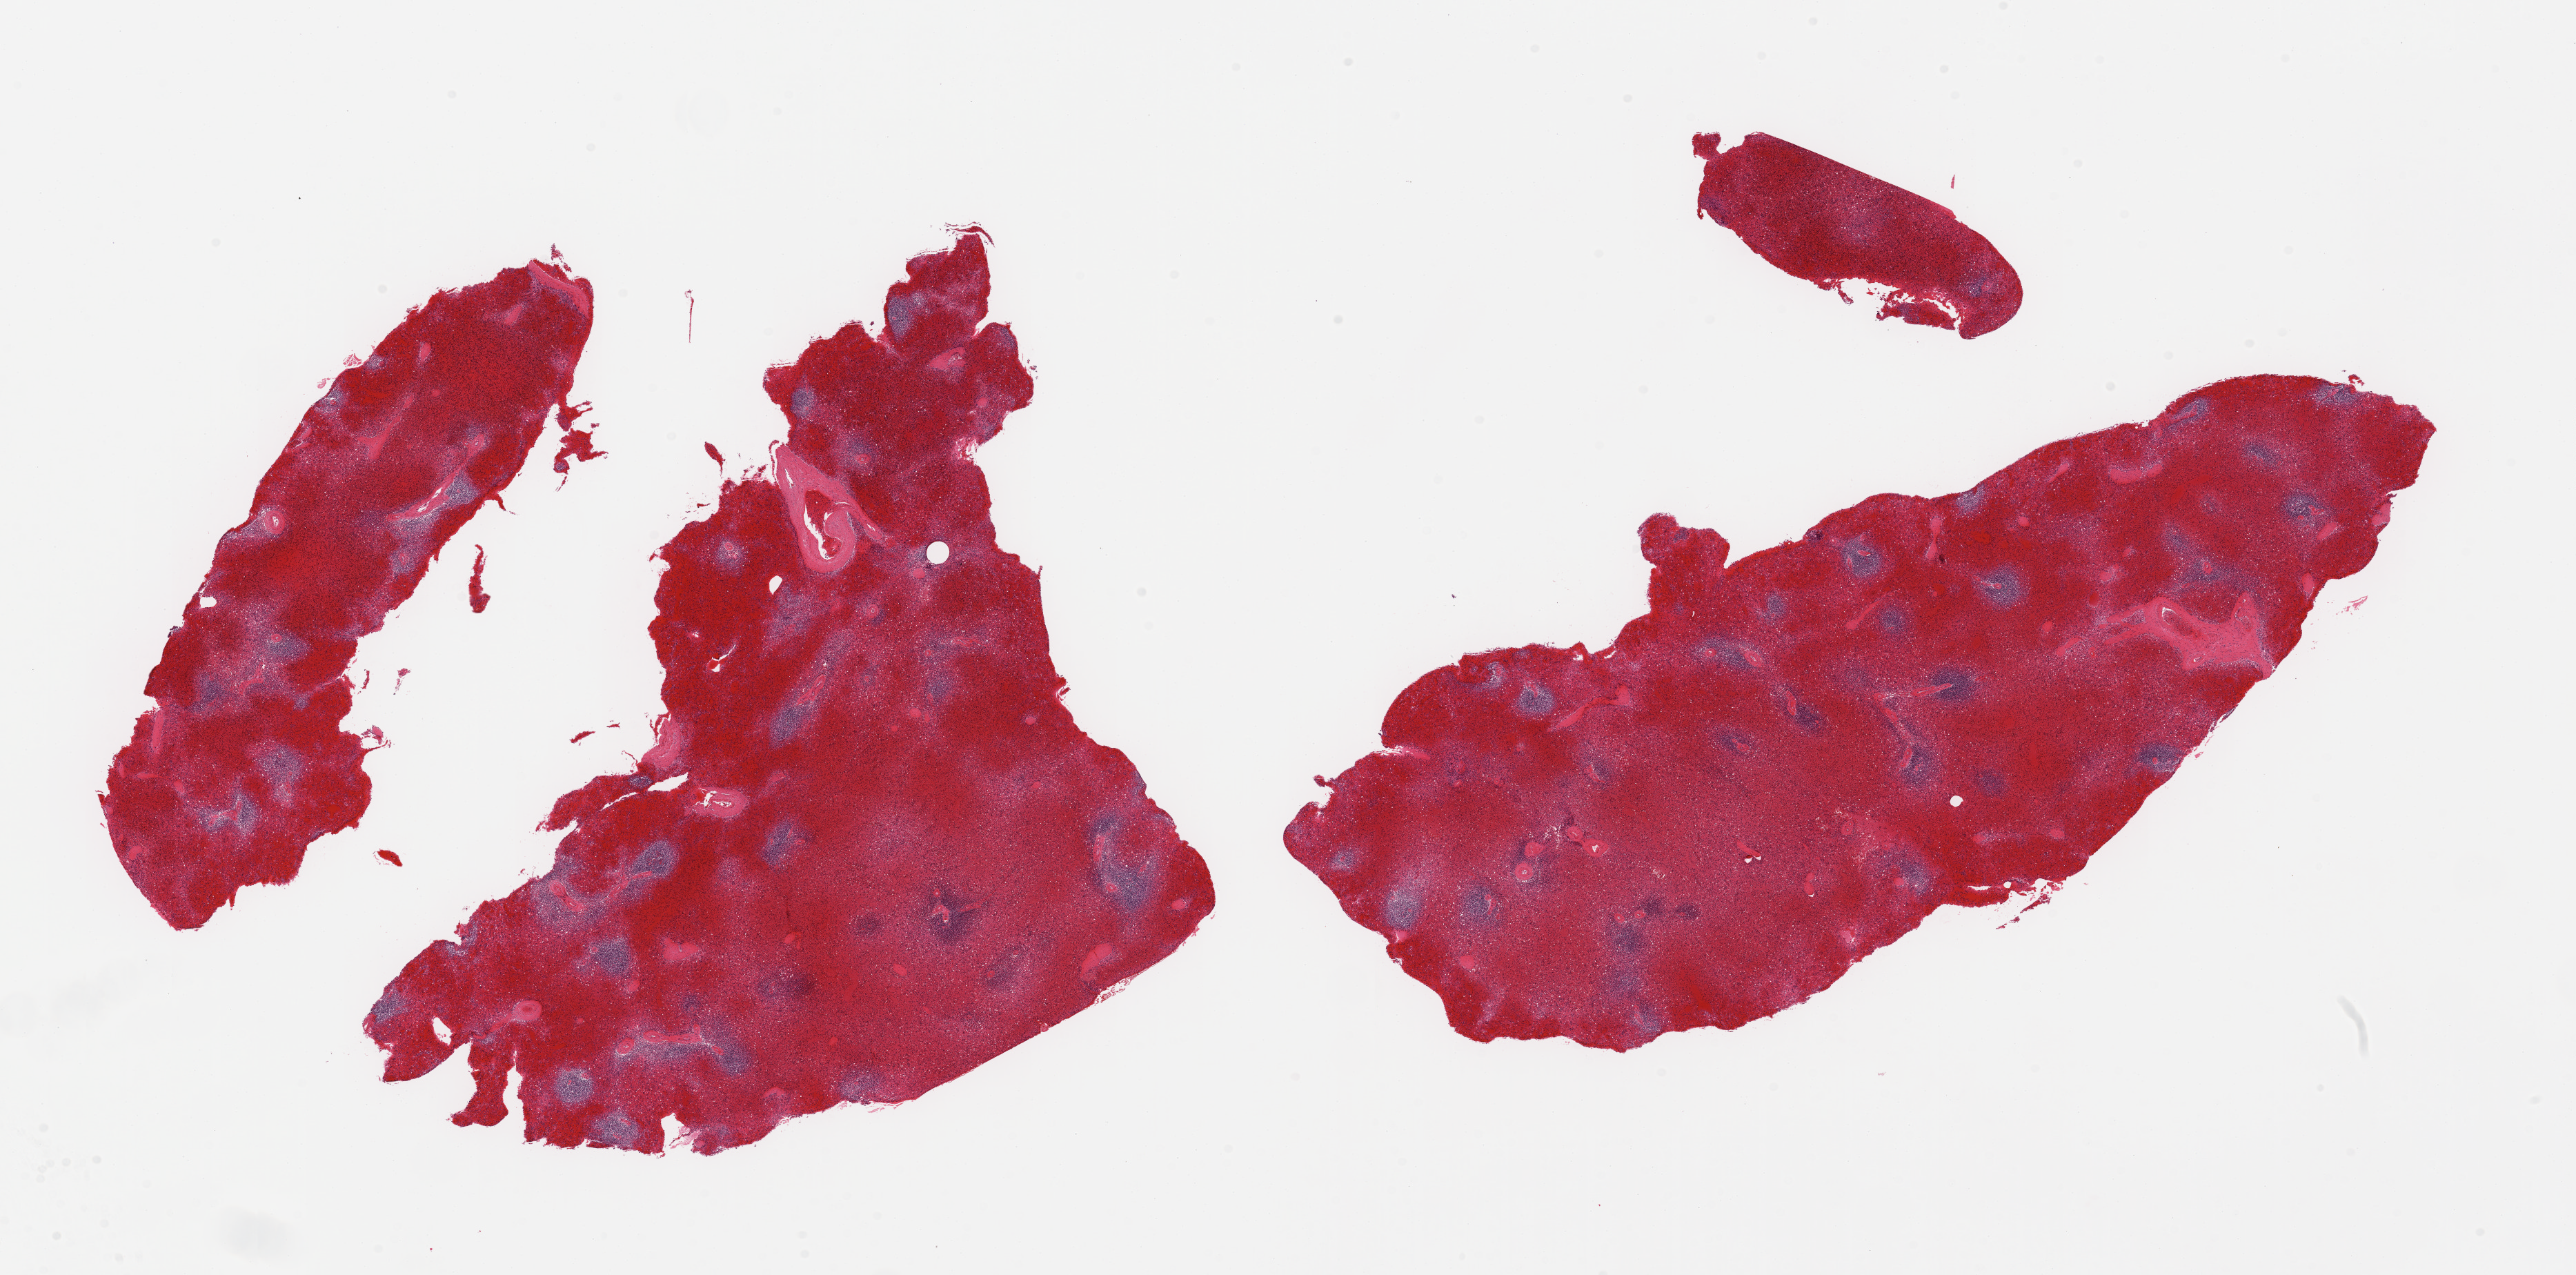
H&E whole-slide image, whole scanned area (about 29.5 x 14.6 mm) shown as a low-resolution overview. PAXgene-fixed paraffin-embedded (PFPE) section. Sampled site (target tissue): spleen. Donor tissue sample. Donor sex: male.
Pathologist's review note for this sample: 2 fragmented pieces; severe red pulp congestion.